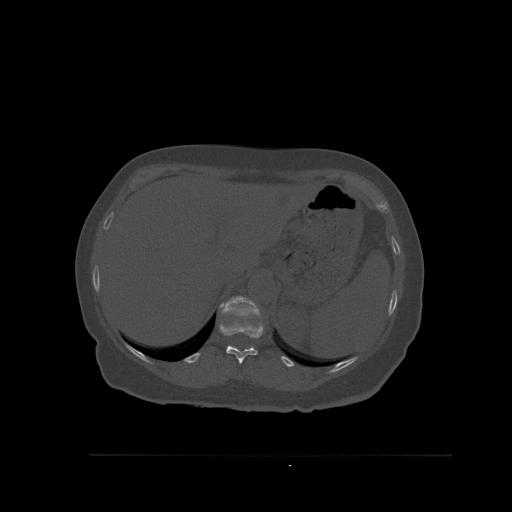
CT including the spine, one axial slice; position 300 of 527 along the scan axis; bone window (W 1800 / L 400 HU); 512 × 512 image matrix, field of view 470 × 470 mm. Patient: female, 73 years. From the clinical record (not read from this slice): primary cancer: breast.
Structures marked on this image (semi-automatic segmentation, software-assisted and operator-edited):
- T11 vertebra: bounding box [x1, y1, x2, y2] px = [219, 322, 264, 364]
- T12 vertebra: [219, 296, 261, 318]